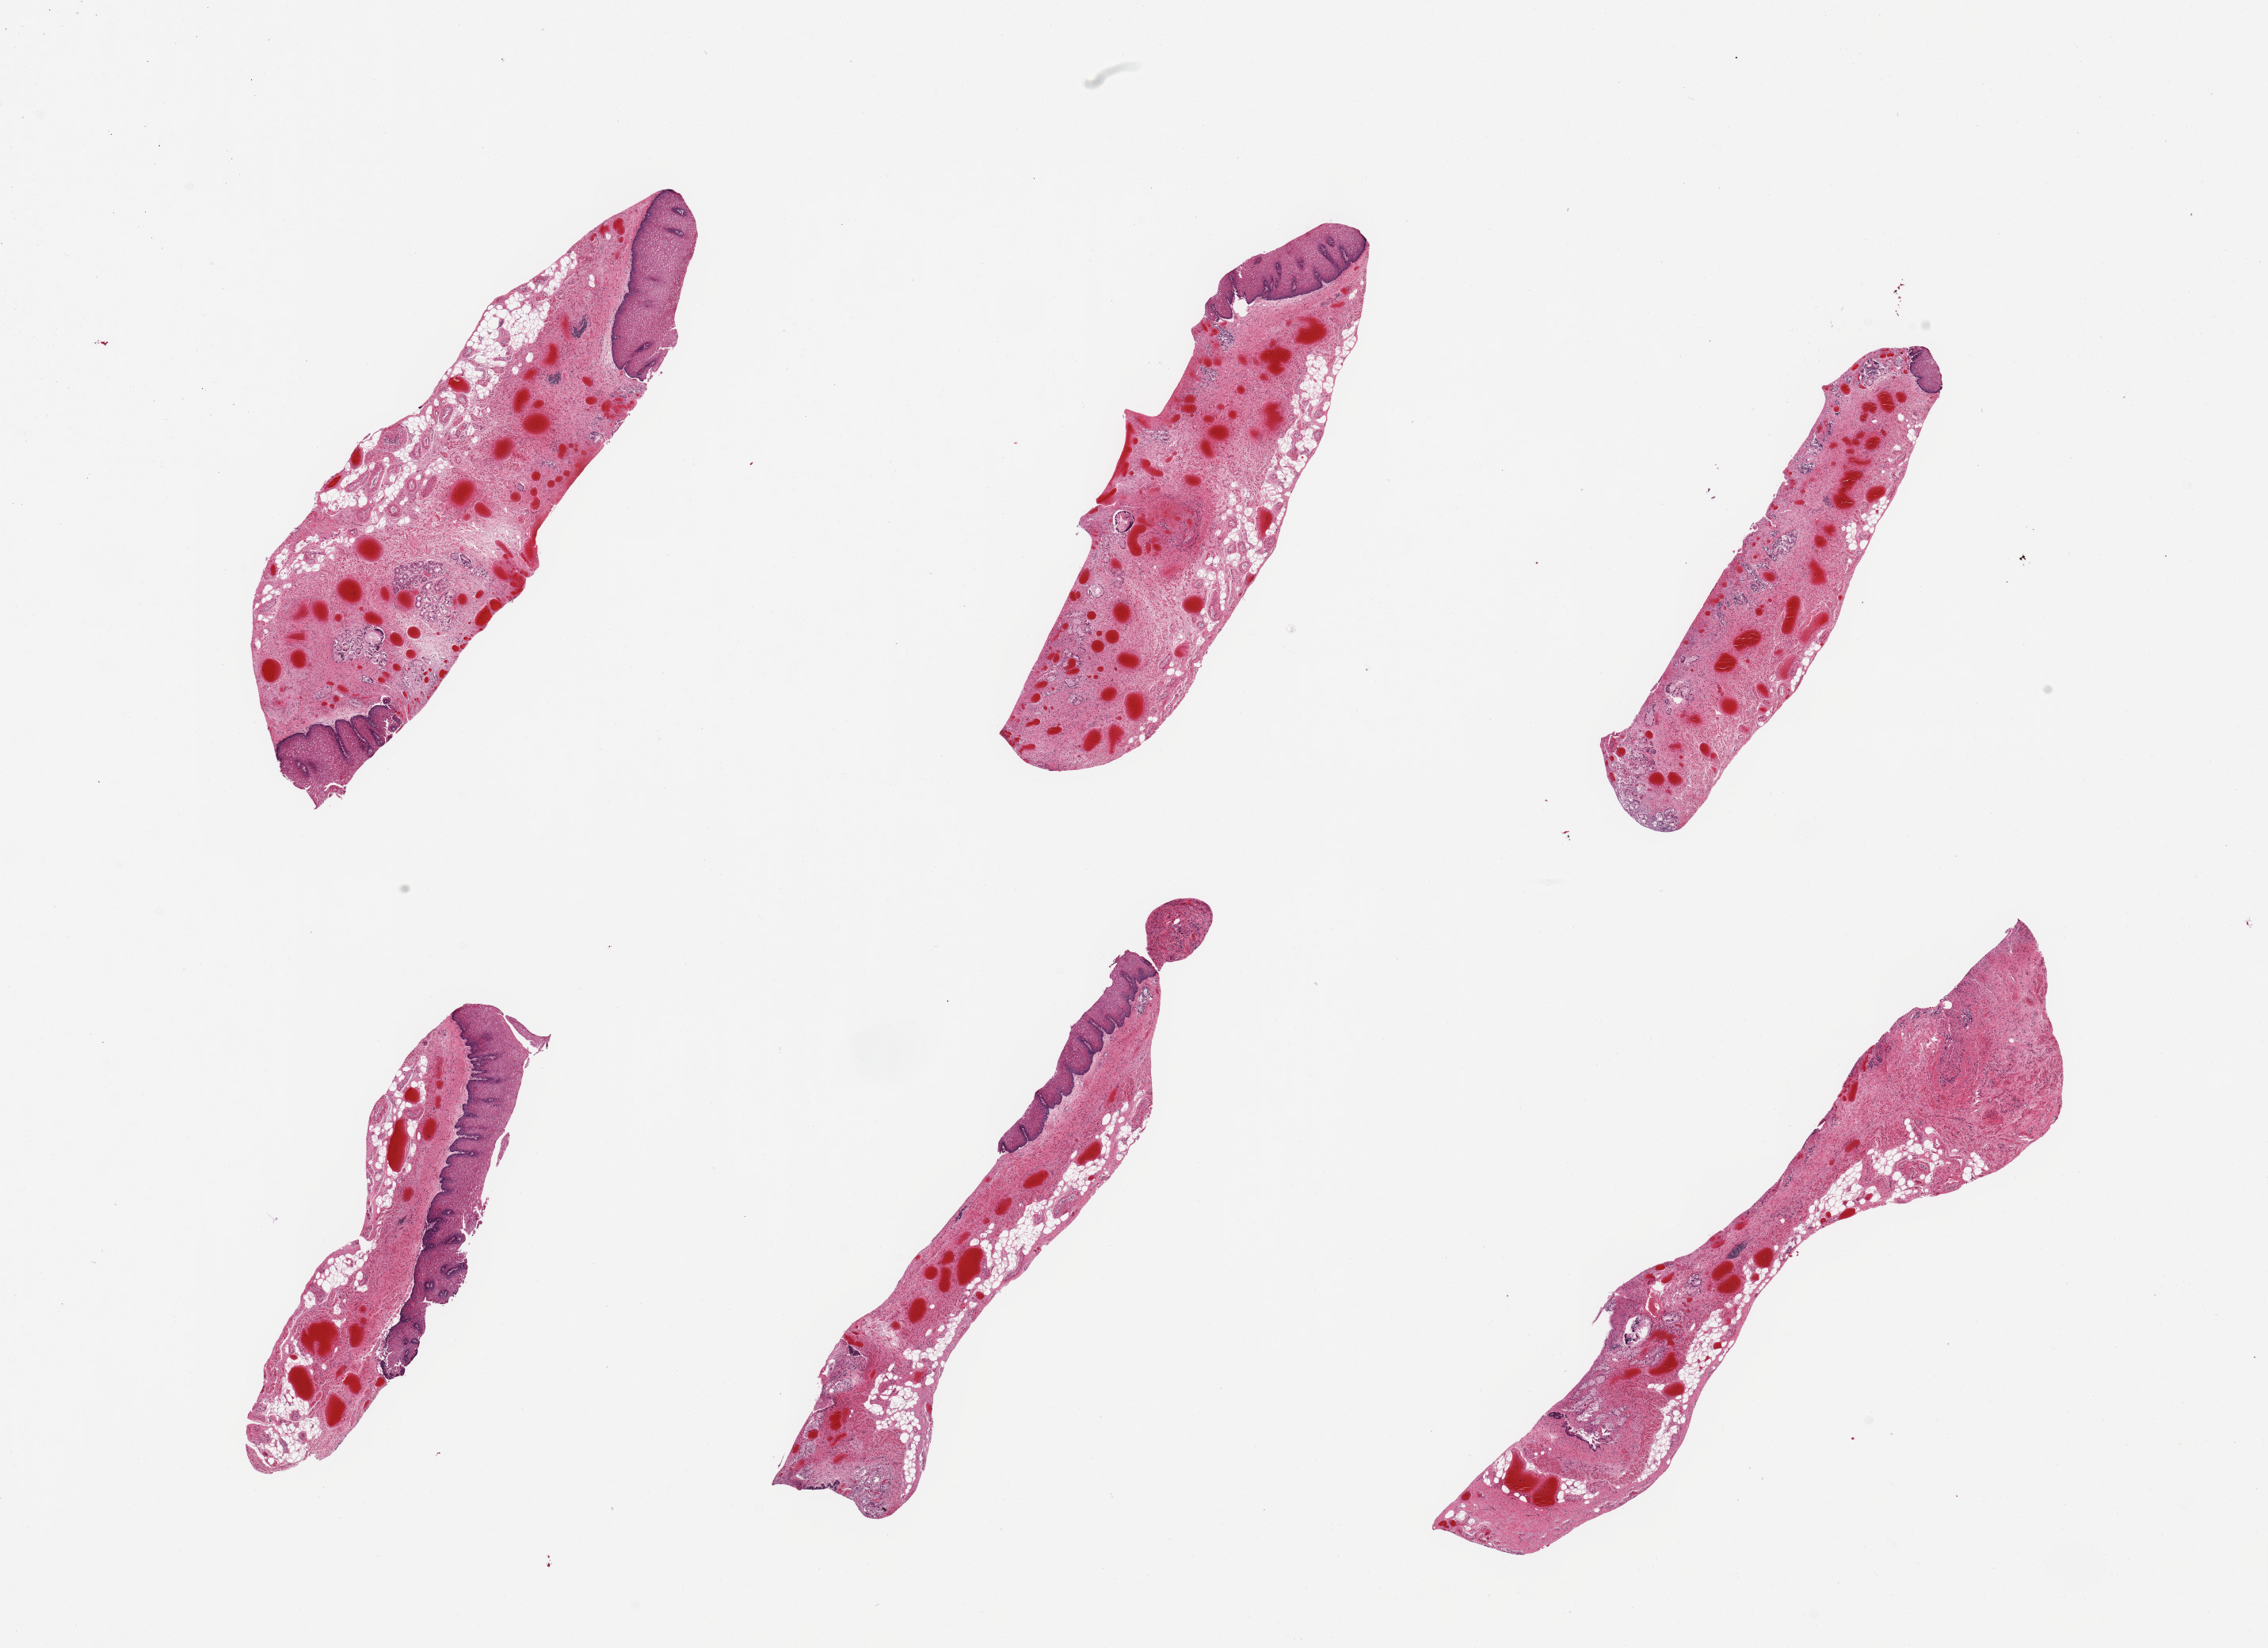
Whole-slide image, haematoxylin and eosin stain — a low-resolution overview of the entire scanned area, about 22.6 x 16.4 mm (acquisition: 20x scan), PAXgene-fixed paraffin-embedded (PFPE) section, target tissue: esophageal mucous membrane, tissue donor sample. Donor sex: male.
• reviewer comment on this tissue sample: 6 pieces; limited amount of squamous lining varying from 0 to 85% coverage; lamina propria moderately congested